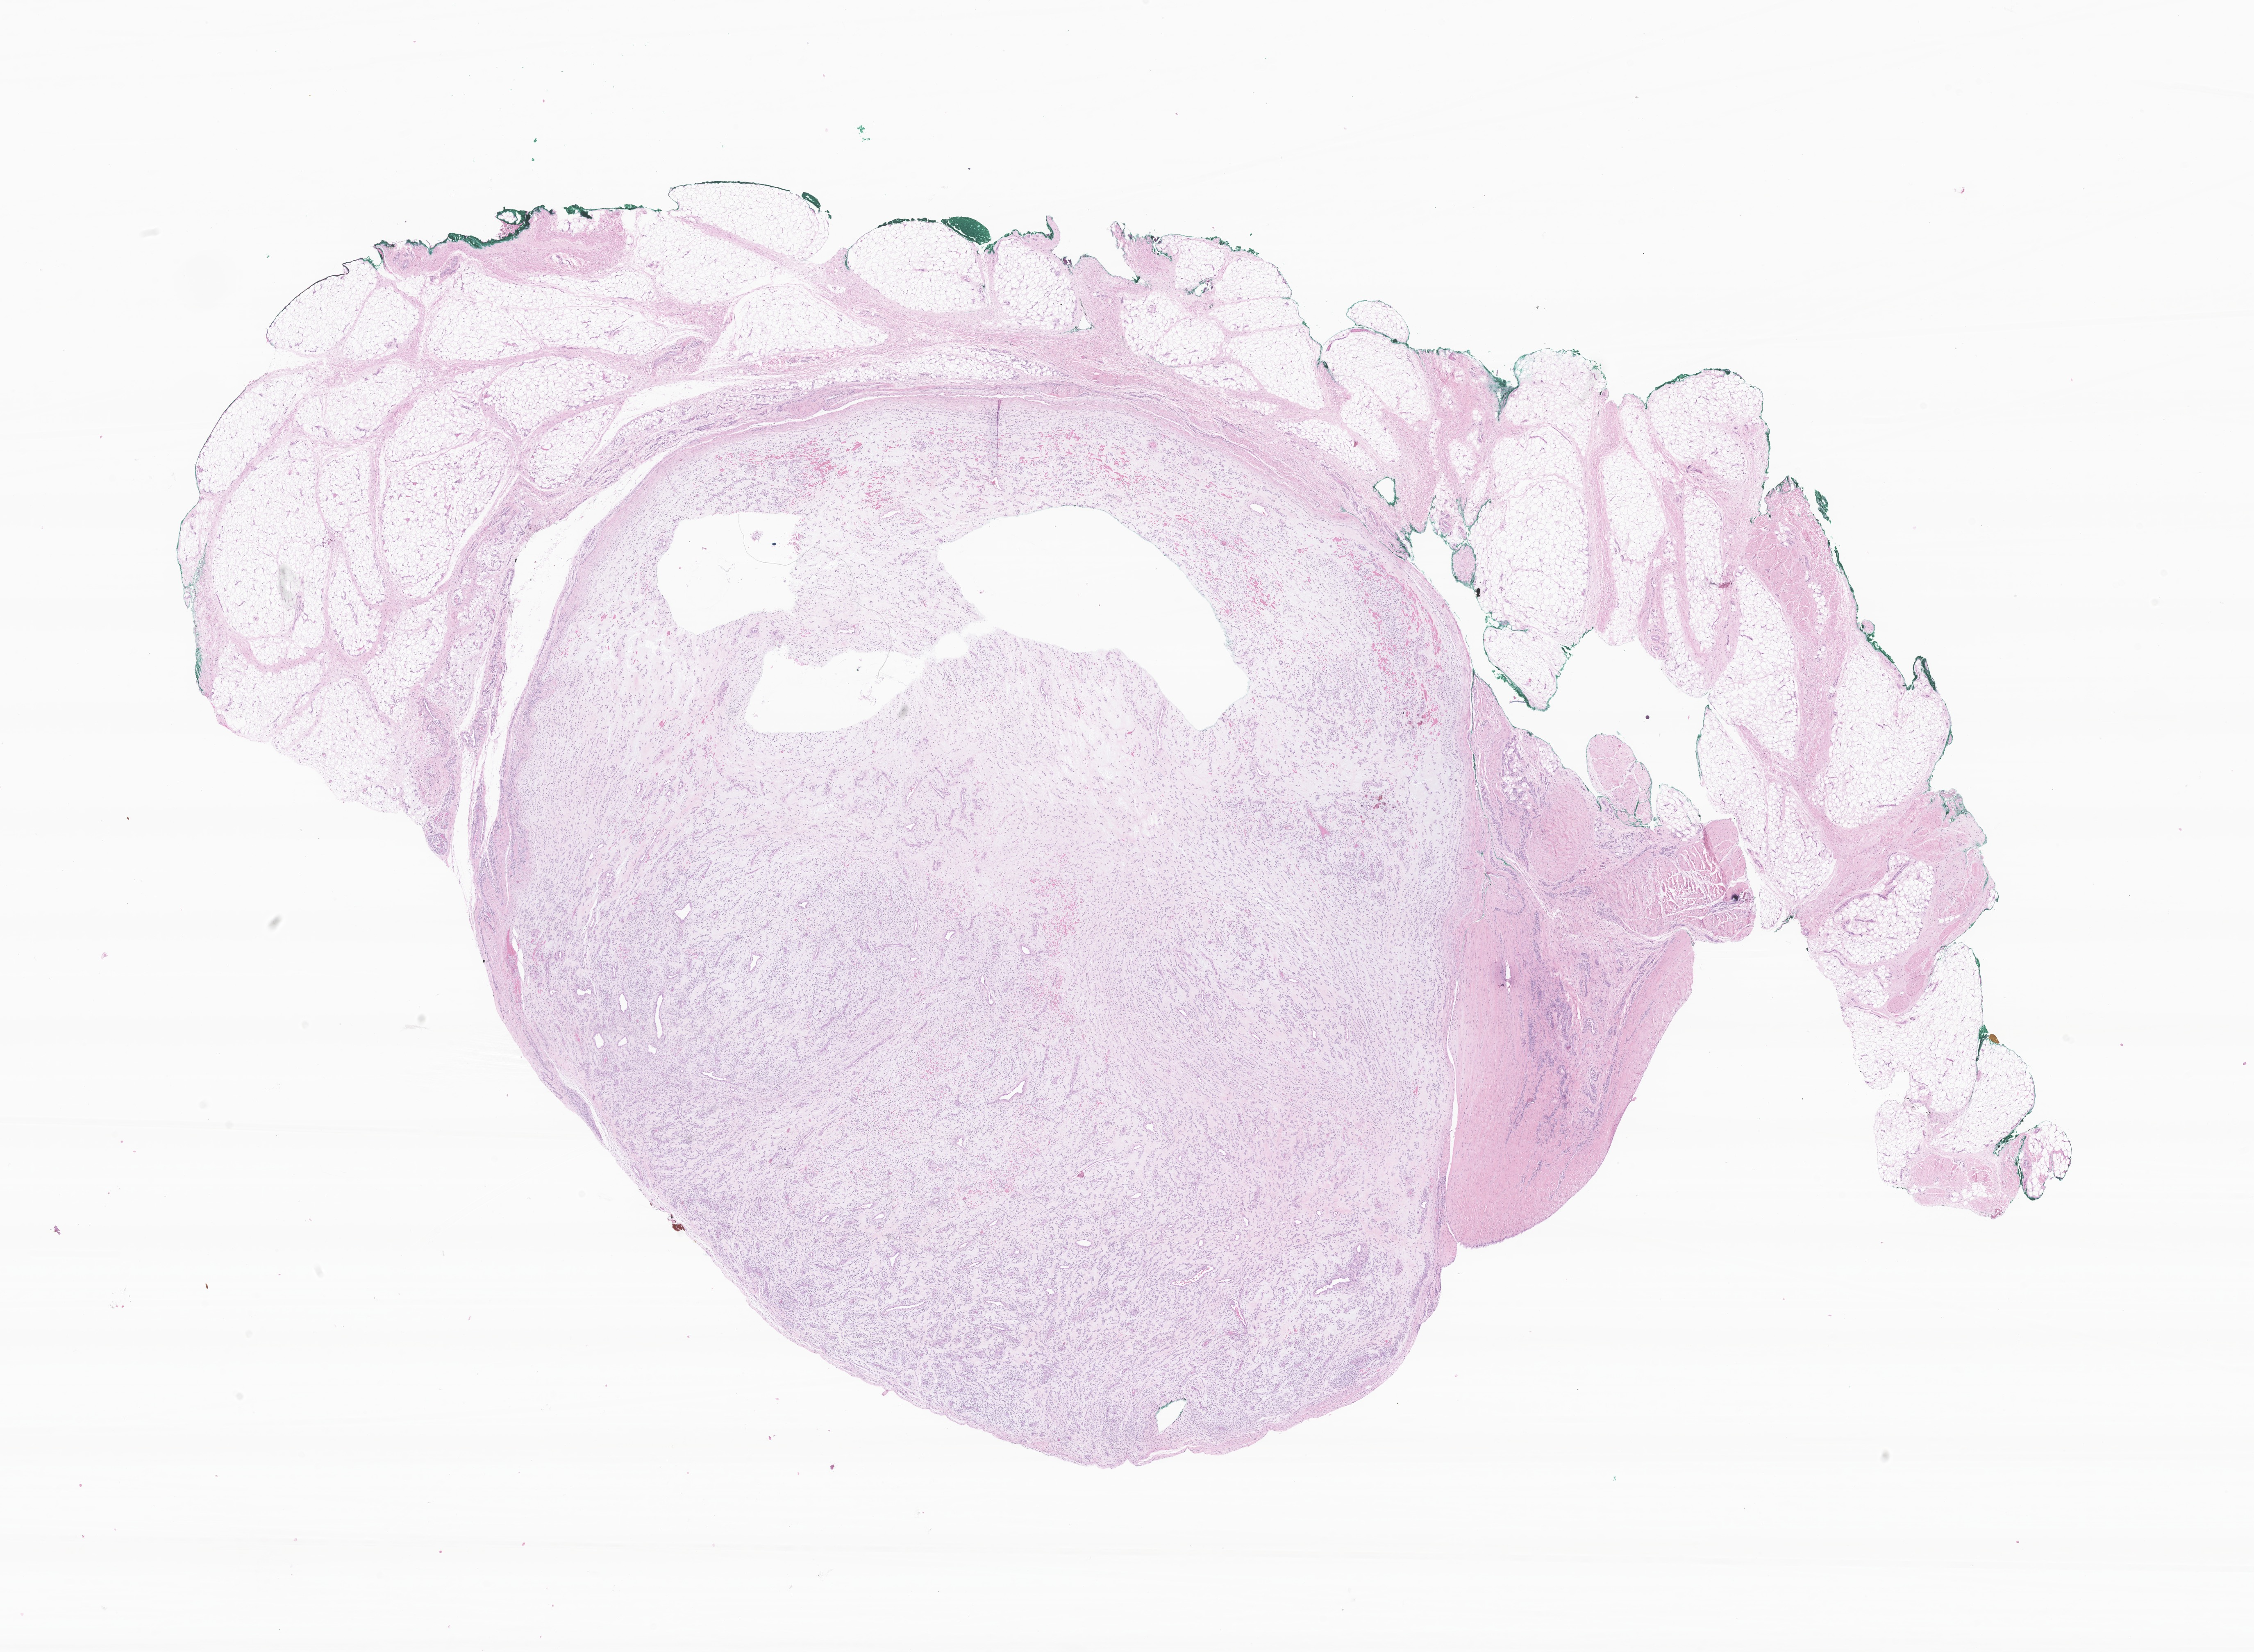
Hematoxylin and eosin (H&E) whole-slide image of tumor tissue from the soft tissue of lower extremity, whole scanned area (about 23.2 x 17.0 mm) shown as a low-resolution overview, FFPE section. Male patient, age 171 months (14 years 3 months).
• tissue or organ of origin (case record): connective, subcutaneous and other soft tissues of lower limb and hip
• diagnosis (ICD-O-3 morphology term): Undifferentiated sarcoma